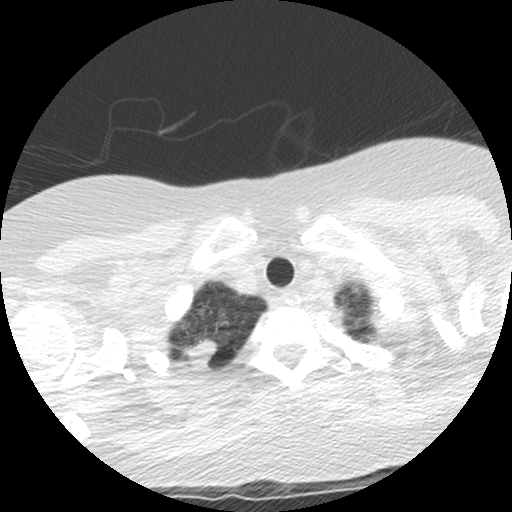
Low-dose screening chest CT, one axial slice; position 121 of 130 along the scan axis; 120 kVp; lung window (W 1500 / L -600 HU); 512 × 512 image matrix.
Outlined on this slice (expert manual segmentation):
- lesion 1 (tumor, upper lobe of right lung): bounding box (x1, y1, x2, y2) in pixels: (185, 341, 216, 365)